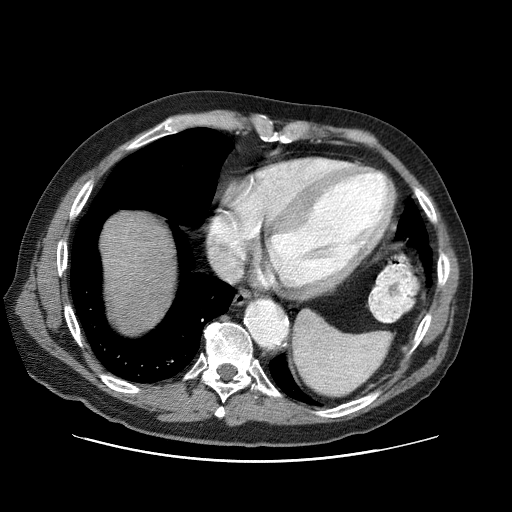
Contrast-enhanced abdominal CT (liver protocol), one axial slice. Reconstruction kernel STANDARD. One of 3 acquisitions stored at this slice position. Soft-tissue window (W 400 / L 40 HU). 2.5 mm slice thickness. 512 × 512 image matrix. From the clinical record (not read from this slice): diagnosis: hepatocellular carcinoma (patient treated with transarterial chemoembolisation; whether this scan precedes or follows treatment is not stated here); TNM stage (as recorded): Stage-IIIA; Child-Pugh class: A; tumour nodularity: multinodular.
Outlined on this slice (semi-automatically segmented with operator editing):
- liver parenchyma outside the tumour (the mass and vessels are separate outlines, so this box may not span the whole liver): box from (x=100, y=210) to (x=176, y=330) px